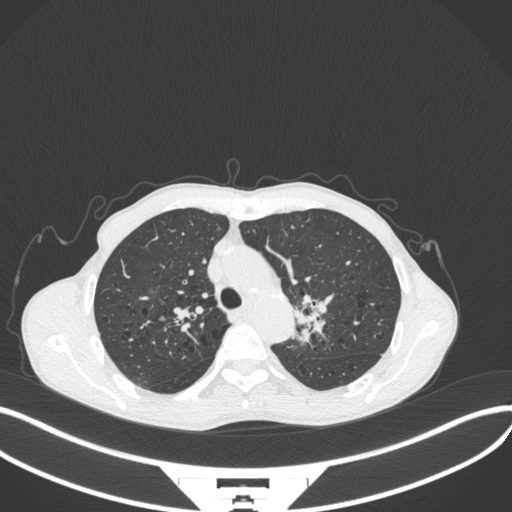
Chest CT, one axial slice; position 305 of 394 along the scan axis; lung window (W 1500 / L -600 HU); 1 mm slice thickness; 512 × 512 image matrix, field of view 400 × 400 mm. Male patient, age 65 years. From the clinical record (not read from this slice): clinical TNM (as recorded): T2b N0 M0.
Outlined on this slice (rectangle marked by the reading radiologist):
- lung tumour (recorded histology: adenocarcinoma): bounding box [x1, y1, x2, y2] px = [294, 289, 337, 349]